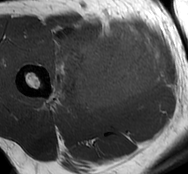
MRI of an extremity soft-tissue mass, one axial slice. Slice 33 of 93 in the series (ordered by position). MR volume resampled by the dataset authors to the PET/CT grid (not the native acquisition matrix). 3.27 mm slice thickness. 188 × 174 image matrix. Male patient. Case-level facts recorded for this patient, not image findings: histological type: undifferentiated - pleiomorphic; grade: high; site of the primary tumour: right thigh.
Outlined on this slice (expert contour drawn on MRI and transferred to this co-registered scan by the dataset authors):
- gross tumour volume including surrounding oedema: bounding box (x1, y1, x2, y2) in pixels: (49, 24, 165, 111)
- gross tumour volume (mass): (72, 26, 165, 111)